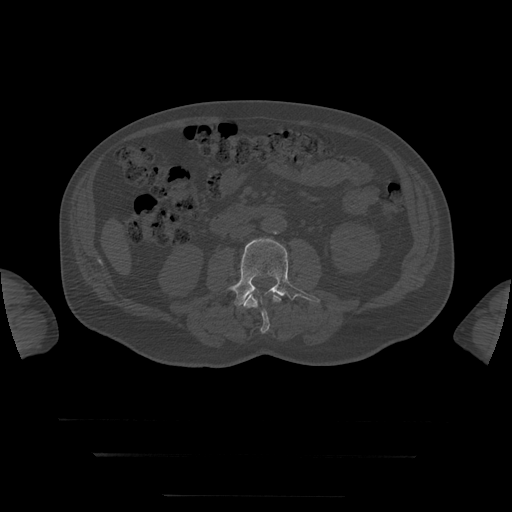
CT including the spine, one axial slice. Position 3 of 397 along the scan axis. Reconstruction kernel STANDARD. 120 kVp. Bone window (W 1800 / L 400 HU). 512 × 512 image matrix, field of view 510 × 510 mm. Patient age 73 years. From the clinical record (not read from this slice): primary cancer: prostate.
Annotated regions visible in this slice (semi-automatic segmentation, software-assisted and operator-edited):
- L3 vertebra: bounding box <231,239,320,307> (left, top, right, bottom; pixels)